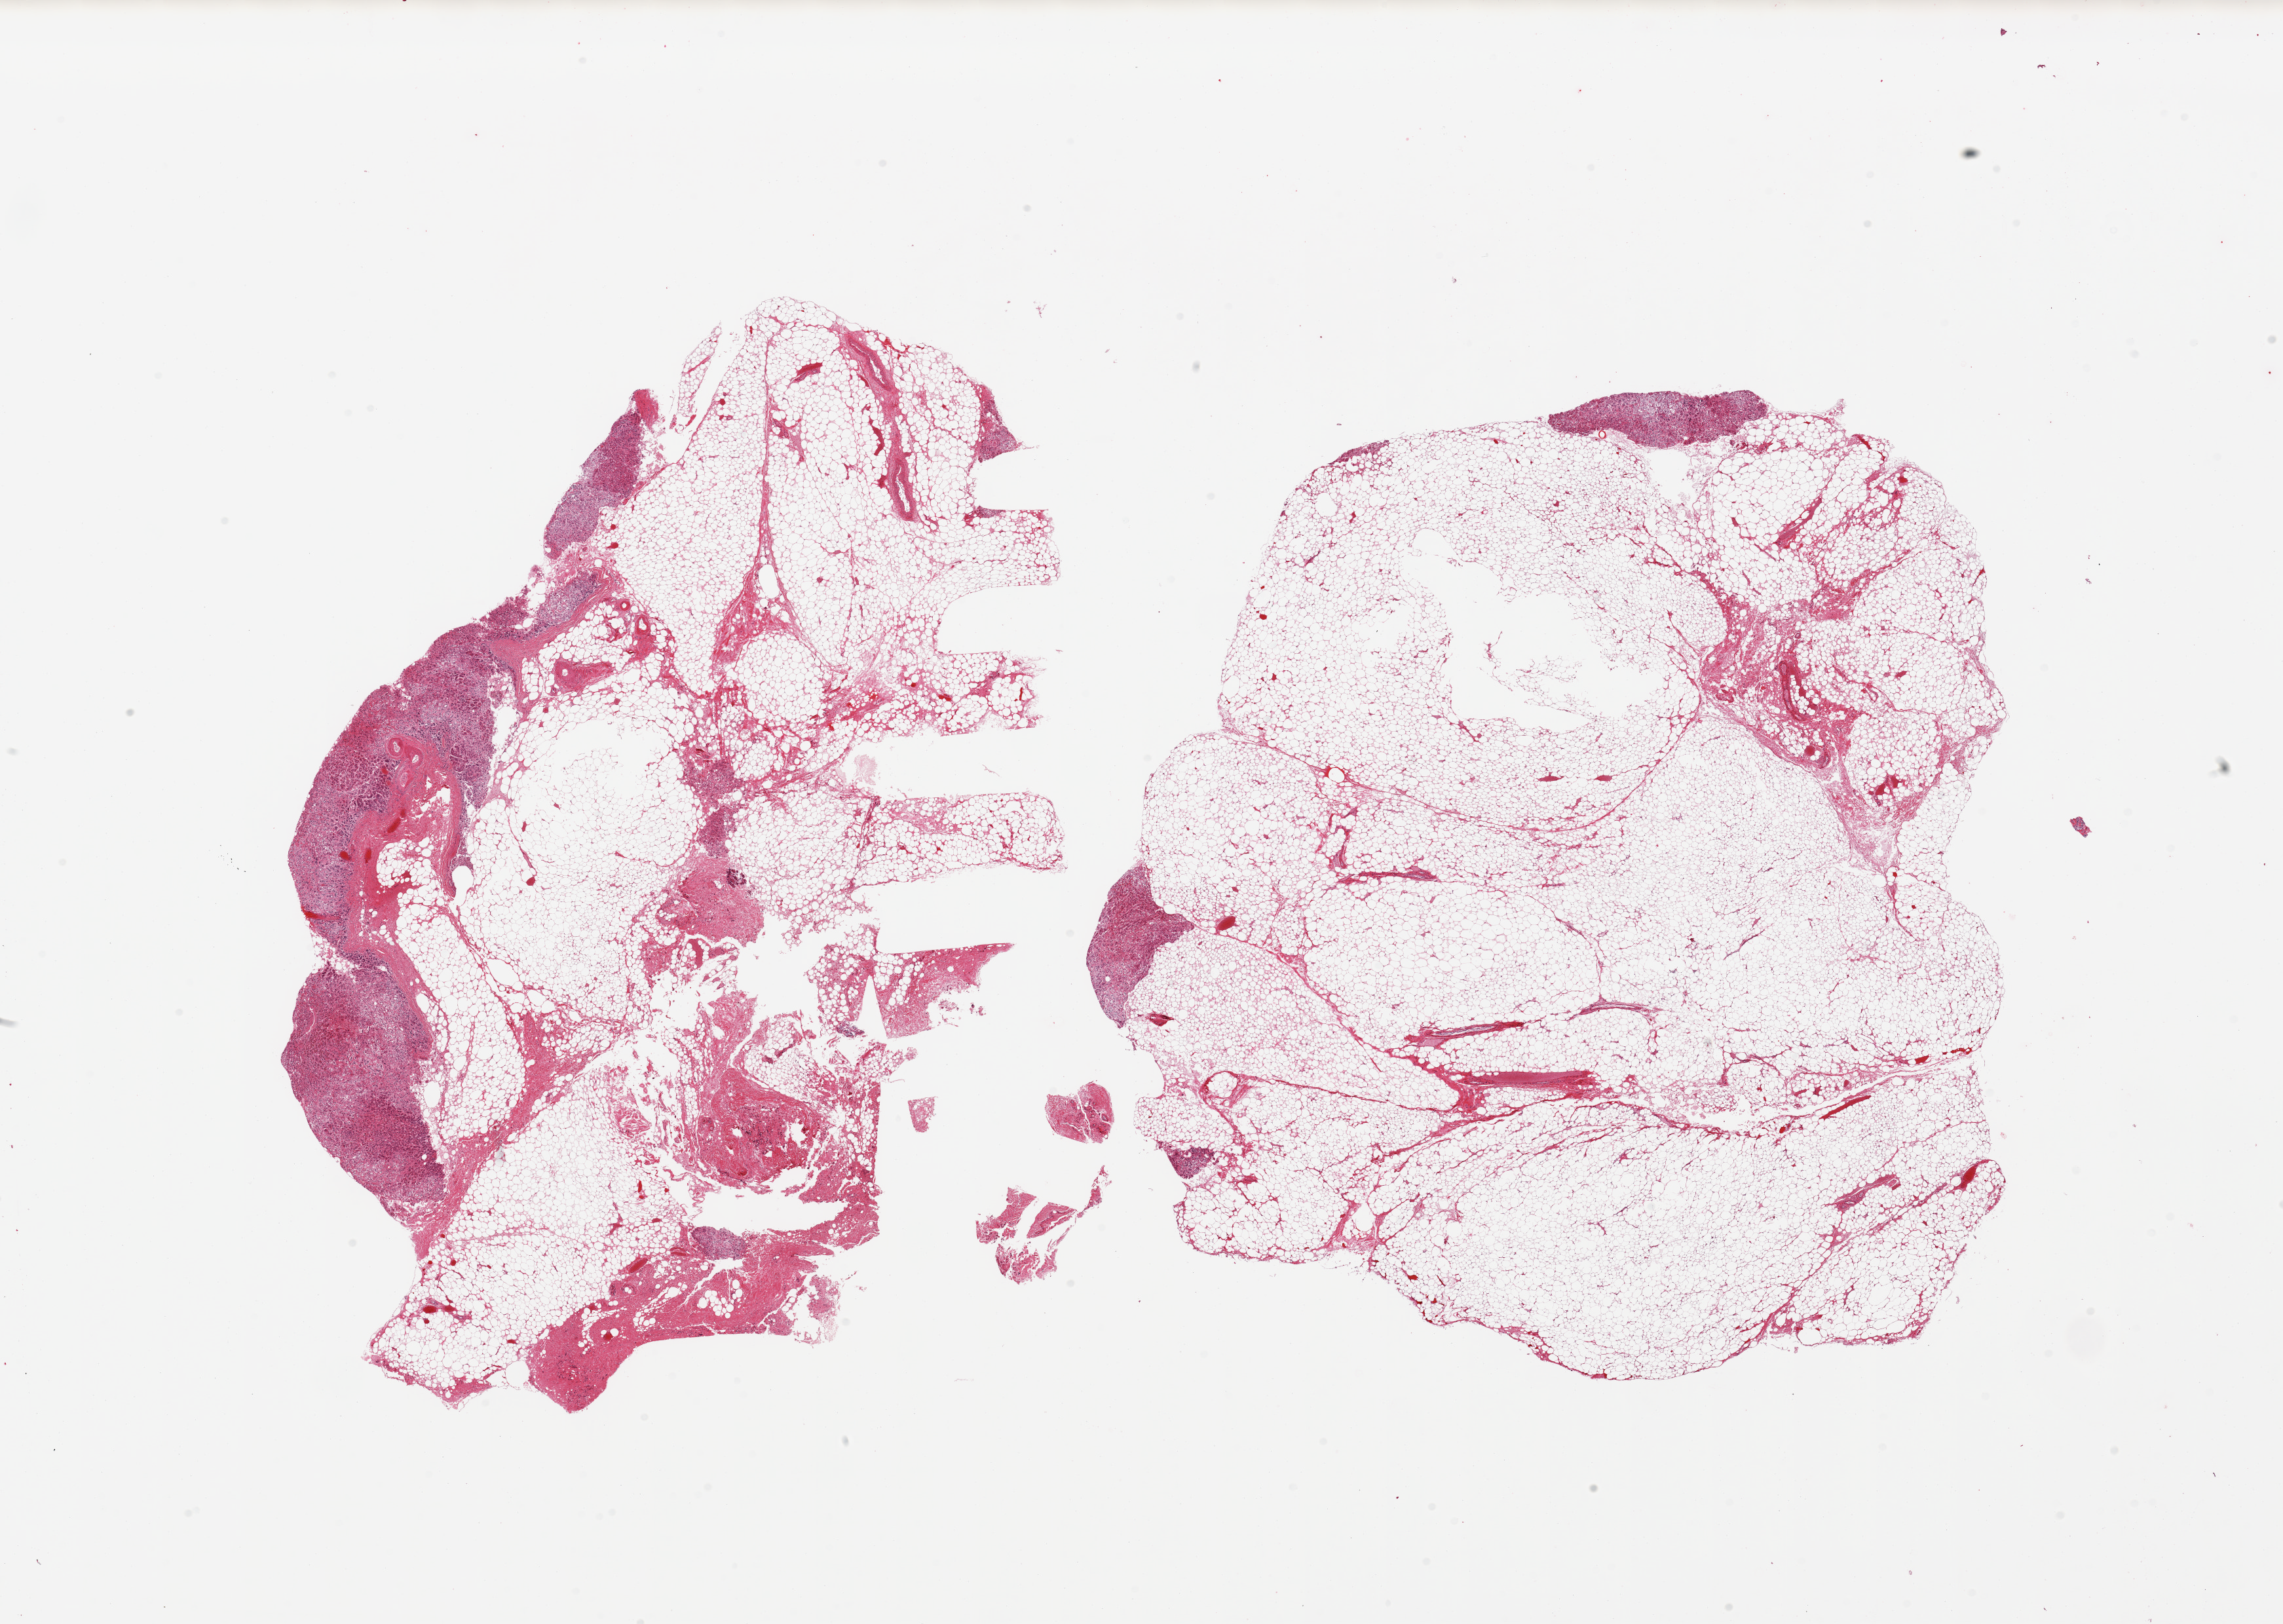
Digitized H&E-stained section, low-resolution overview of the scanned area, about 27.6 x 19.6 mm. Donor sex: male.
Specimen: PAXgene-fixed, paraffin-embedded tissue; sampled site (target tissue): adrenal gland; tissue donor sample.